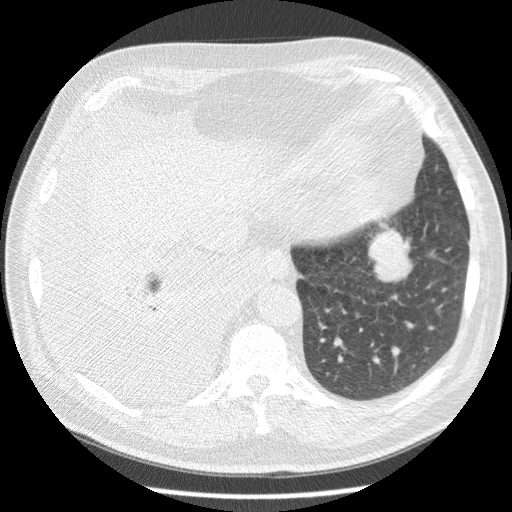
Low-dose screening chest CT, one axial slice. Slice 53 of 180 in the series (ordered by position). Reconstruction kernel STANDARD. 120 kVp. Lung window (W 1500 / L -600 HU). 2.5 mm slice thickness. 512 × 512 image matrix.
Structures marked on this image (manually delineated by an expert):
- lesion 1 (tumor, lower lobe of left lung): bounding box [x1, y1, x2, y2] px = [368, 227, 412, 282]